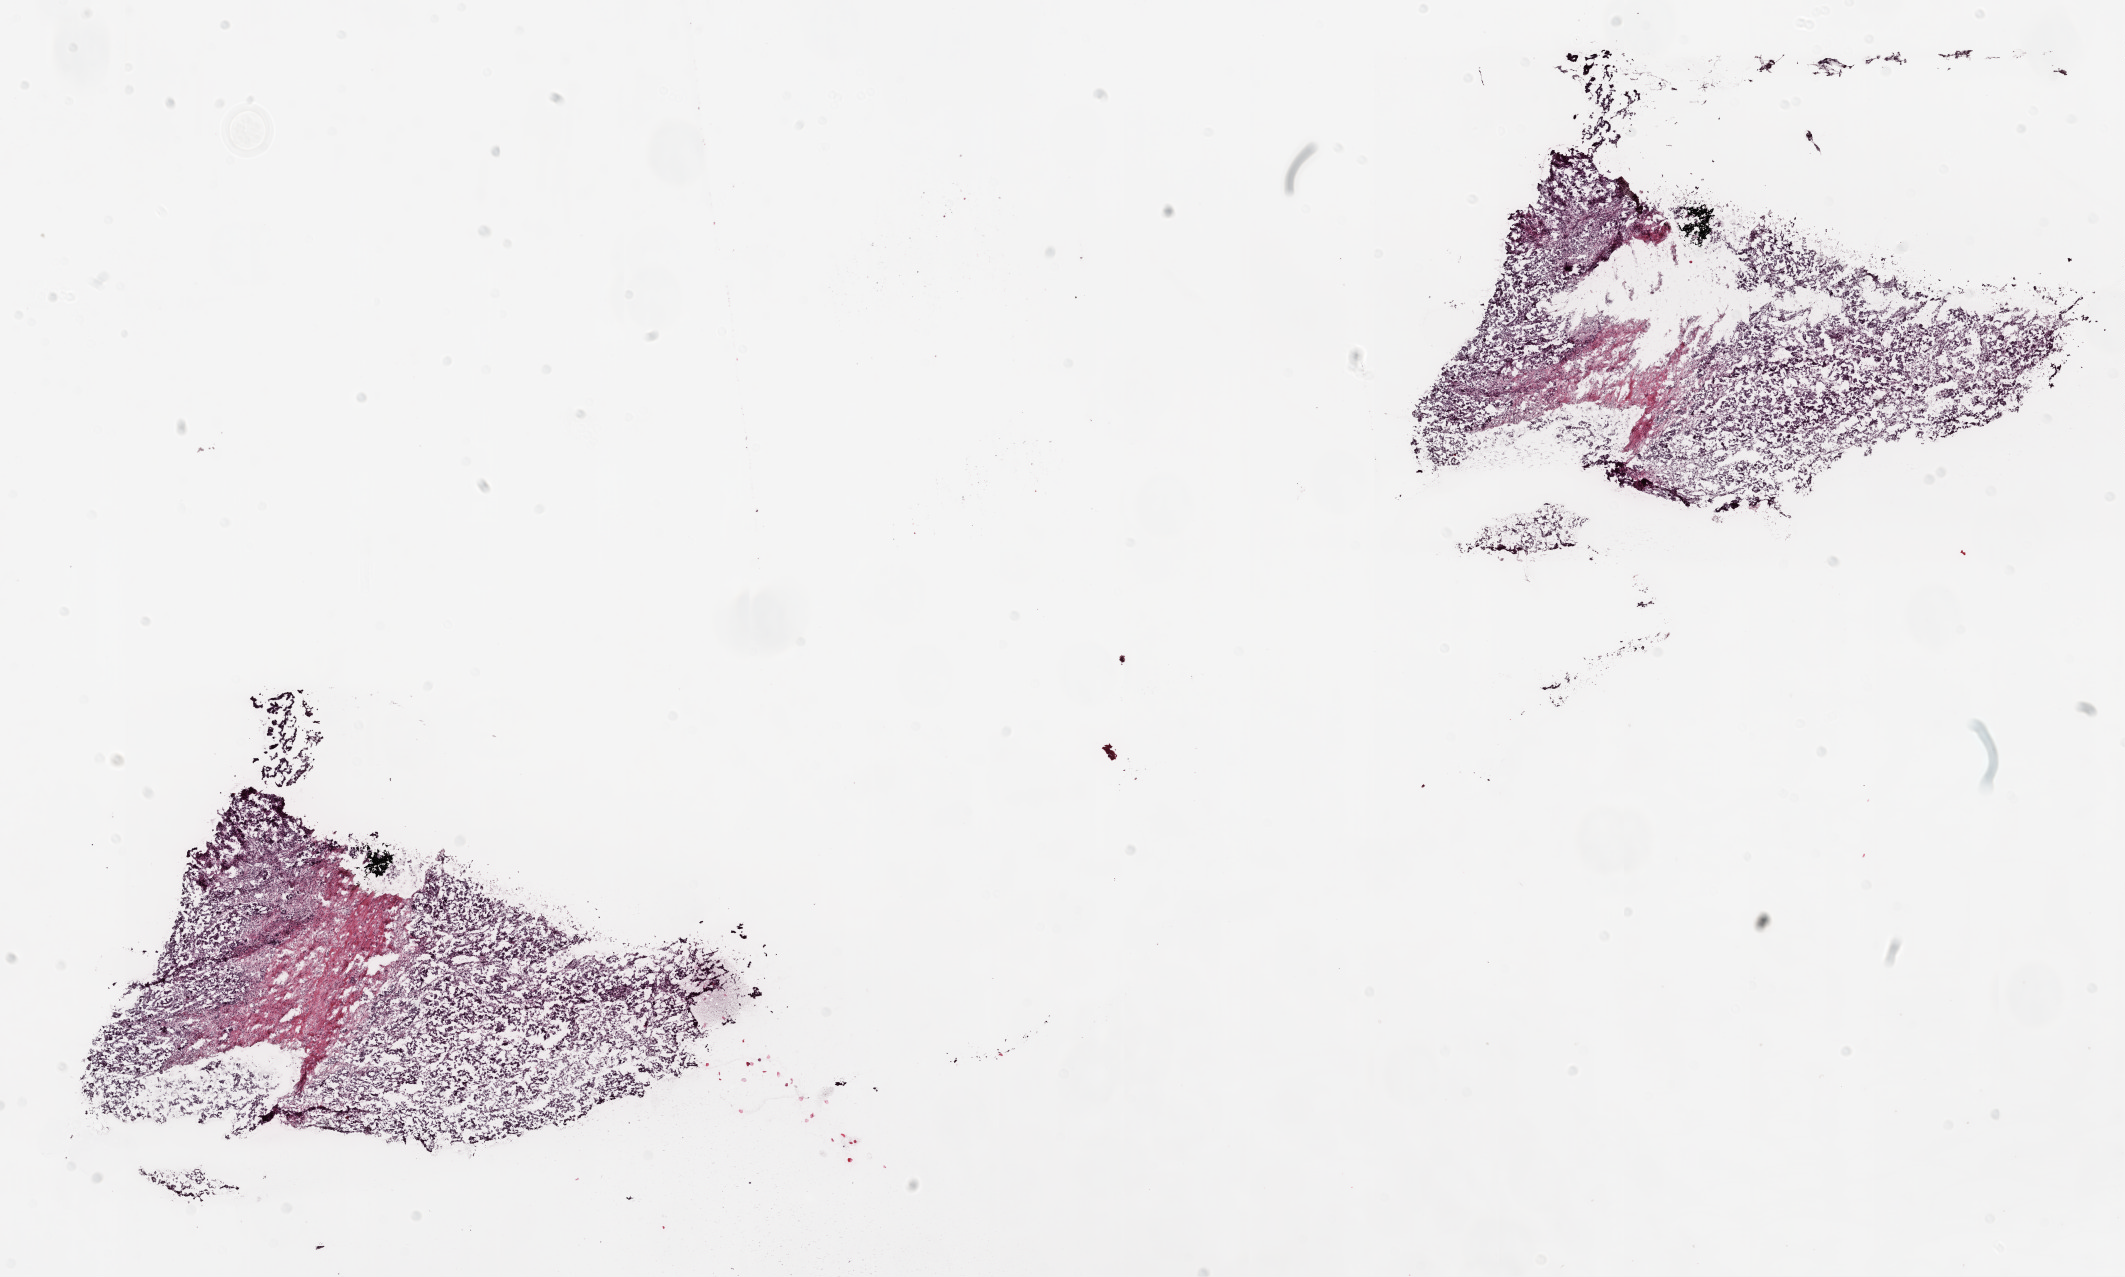
Digitized Hematoxylin and eosin (H&E) stained tissue section (whole slide), whole scanned area (about 17.1 x 10.2 mm, slide scanned at 20x) shown as a low-resolution overview, frozen section from the top of the tissue portion, ovary, primary tumour sample. Female patient; age at initial diagnosis 74 years. Histologic grade: G3 (poorly differentiated). Pathologist review of this section (percent, as recorded): tumour cells 75%, tumour nuclei 80%, normal cells 0%, stromal cells 25%, necrosis 0%.
* diagnosis: Serous cystadenocarcinoma, NOS
* FIGO stage: IIIC